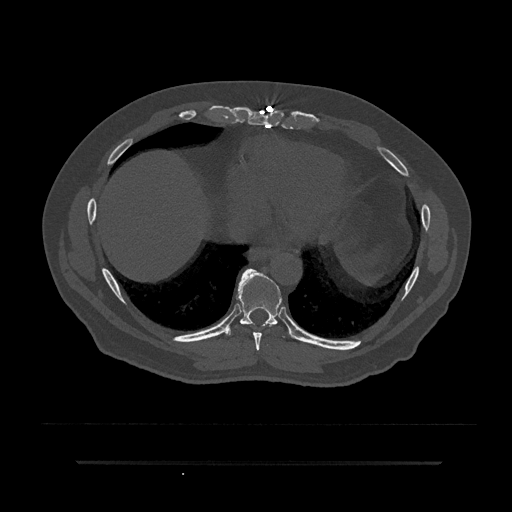
CT including the spine, one axial slice. Slice 398 of 797 in the series (ordered by position). 120 kVp. Bone window (W 1800 / L 400 HU). 512 × 512 image matrix, field of view 464 × 464 mm. Patient: male, 59 years. Case-level facts recorded for this patient, not image findings: primary cancer: bile ducts.
Outlined on this slice (semi-automatic segmentation, software-assisted and operator-edited):
- T8 vertebra: bounding box (x1, y1, x2, y2) in pixels: (253, 332, 262, 351)
- T9 vertebra: (226, 268, 285, 338)